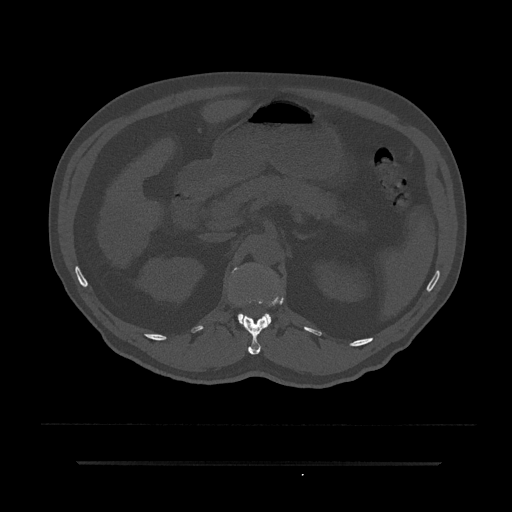
CT including the spine, one axial slice. Position 183 of 797 along the scan axis. Bone window (W 1800 / L 400 HU). 0.5 mm slice thickness. 512 × 512 image matrix, field of view 464 × 464 mm. Patient: male, 59 years. From the clinical record (not read from this slice): primary cancer: bile ducts.
Outlined on this slice (semi-automatically segmented with operator editing):
- L1 vertebra: bounding box [x1, y1, x2, y2] px = [234, 268, 271, 324]
- T12 vertebra: [241, 293, 284, 355]